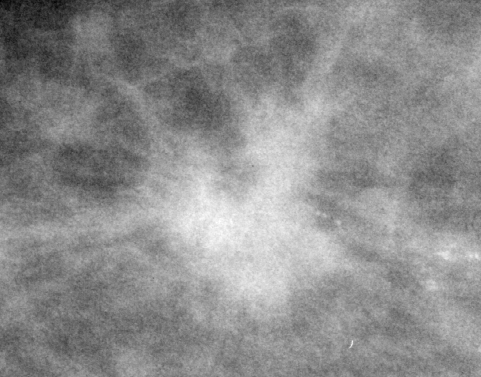
Crop from a digitized film mammogram around one marked abnormality; right breast; CC view; BI-RADS breast density category 1 (scale 1–4).
Calcifications, morphology fine linear branching, distribution clustered / linear; BI-RADS assessment category 5; subtlety rating 4 on a 1 (subtle) to 5 (obvious) scale; pathology result (as recorded, not read from the image): malignant.